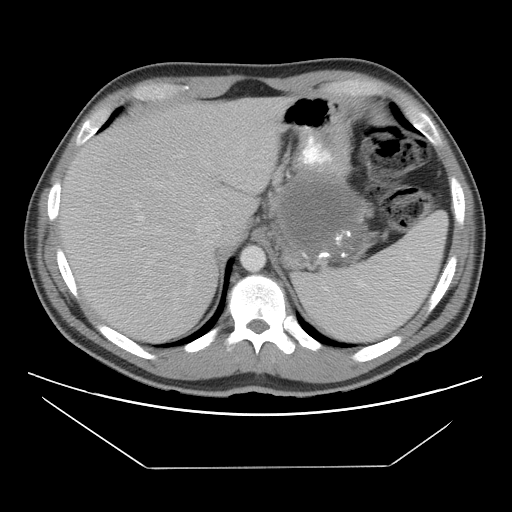
Contrast-enhanced abdominal CT, one axial slice; position 80 of 131 along the scan axis; reconstruction kernel STANDARD; 120 kVp; intravenous contrast given; soft-tissue window (W 400 / L 40 HU); 512 × 512 image matrix. Patient: male, 44 years. Case-level facts recorded for this patient, not image findings: diagnosis: adrenocortical carcinoma; tumour side: left adrenal; tumour size at pathology: 15.5 cm; Ki-67 index: 6 %; stage (as recorded): 2.
Outlined on this slice (semi-automatically segmented with operator editing):
- mass: bounding box (x1, y1, x2, y2) in pixels: (283, 180, 359, 254)